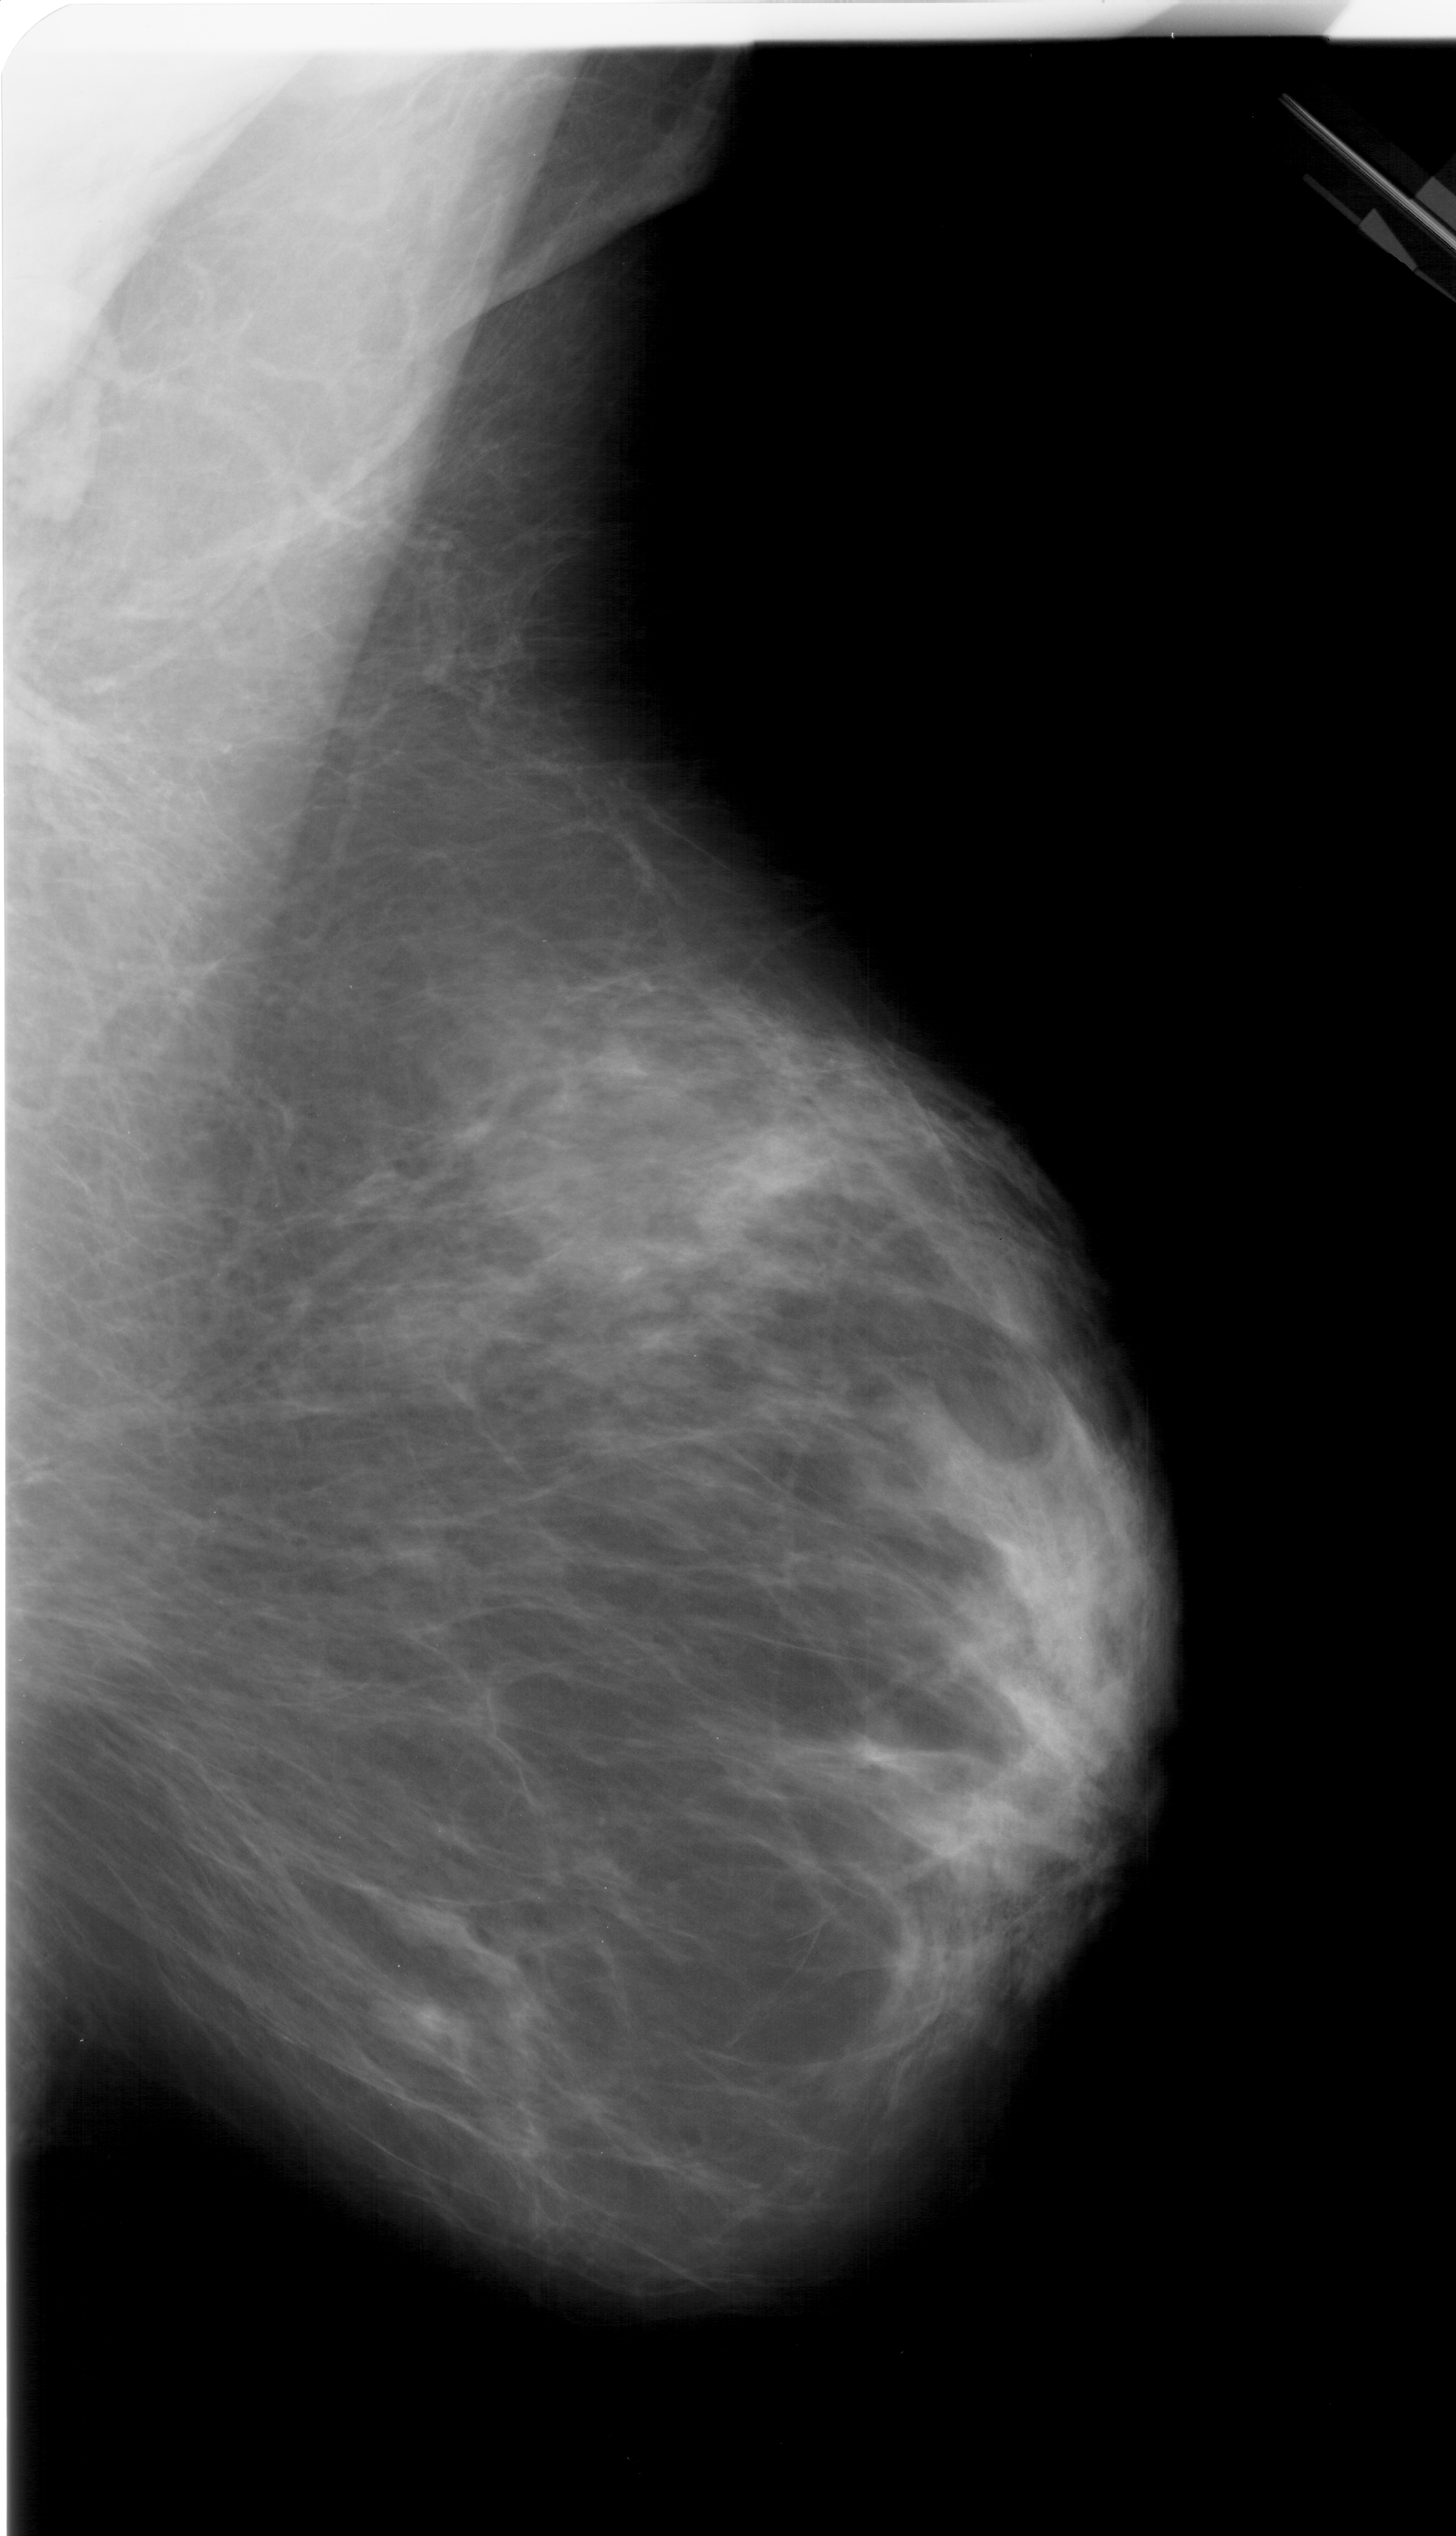
Scanned film-screen mammogram; right breast; mediolateral oblique (MLO) view; breast composition: heterogeneously dense (BI-RADS density category 3 of 4).
- Finding: mass, shape oval, margins circumscribed; BI-RADS assessment category 4; subtlety rating 3 on a 1 (subtle) to 5 (obvious) scale; pathology result (as recorded, not read from the image): benign.